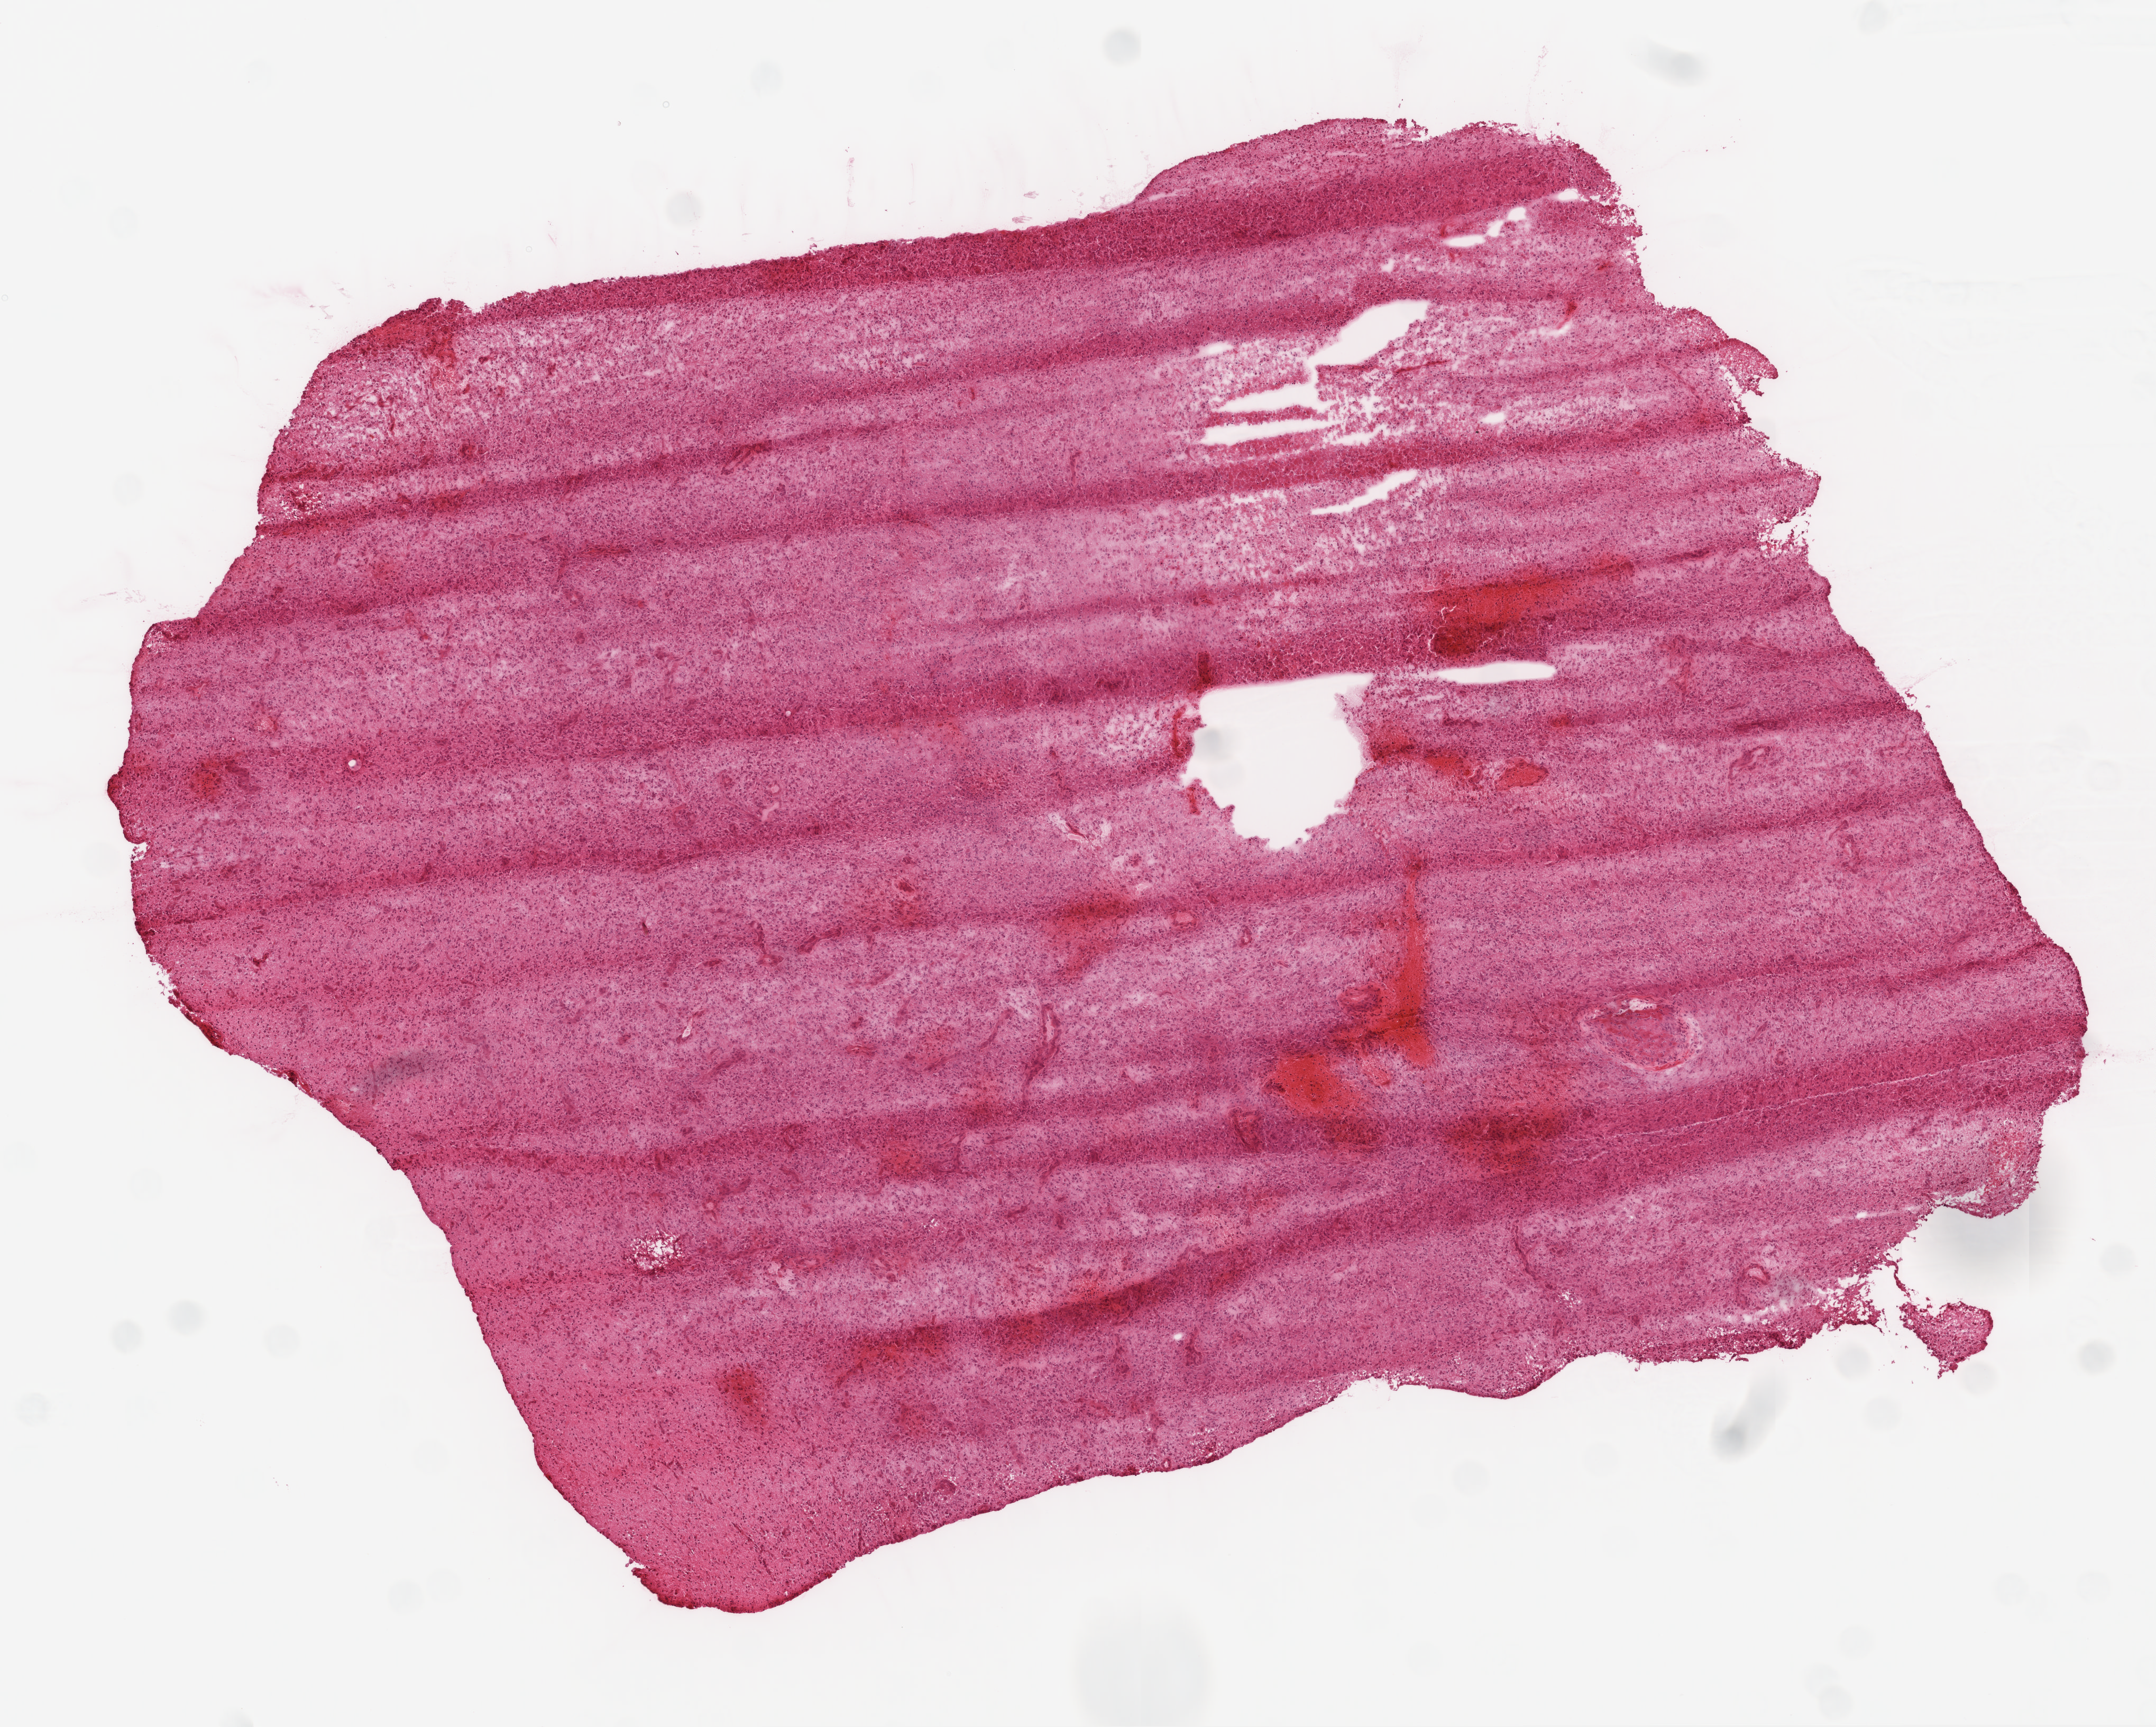
Digitized H&E-stained tissue section (whole slide), a low-resolution overview of the entire scanned area, about 8.2 x 6.6 mm (from a 20x scan); frozen section; primary tumour sample from the brain. Male patient; age at initial diagnosis 57 years.
Pathologic diagnosis: Glioblastoma.